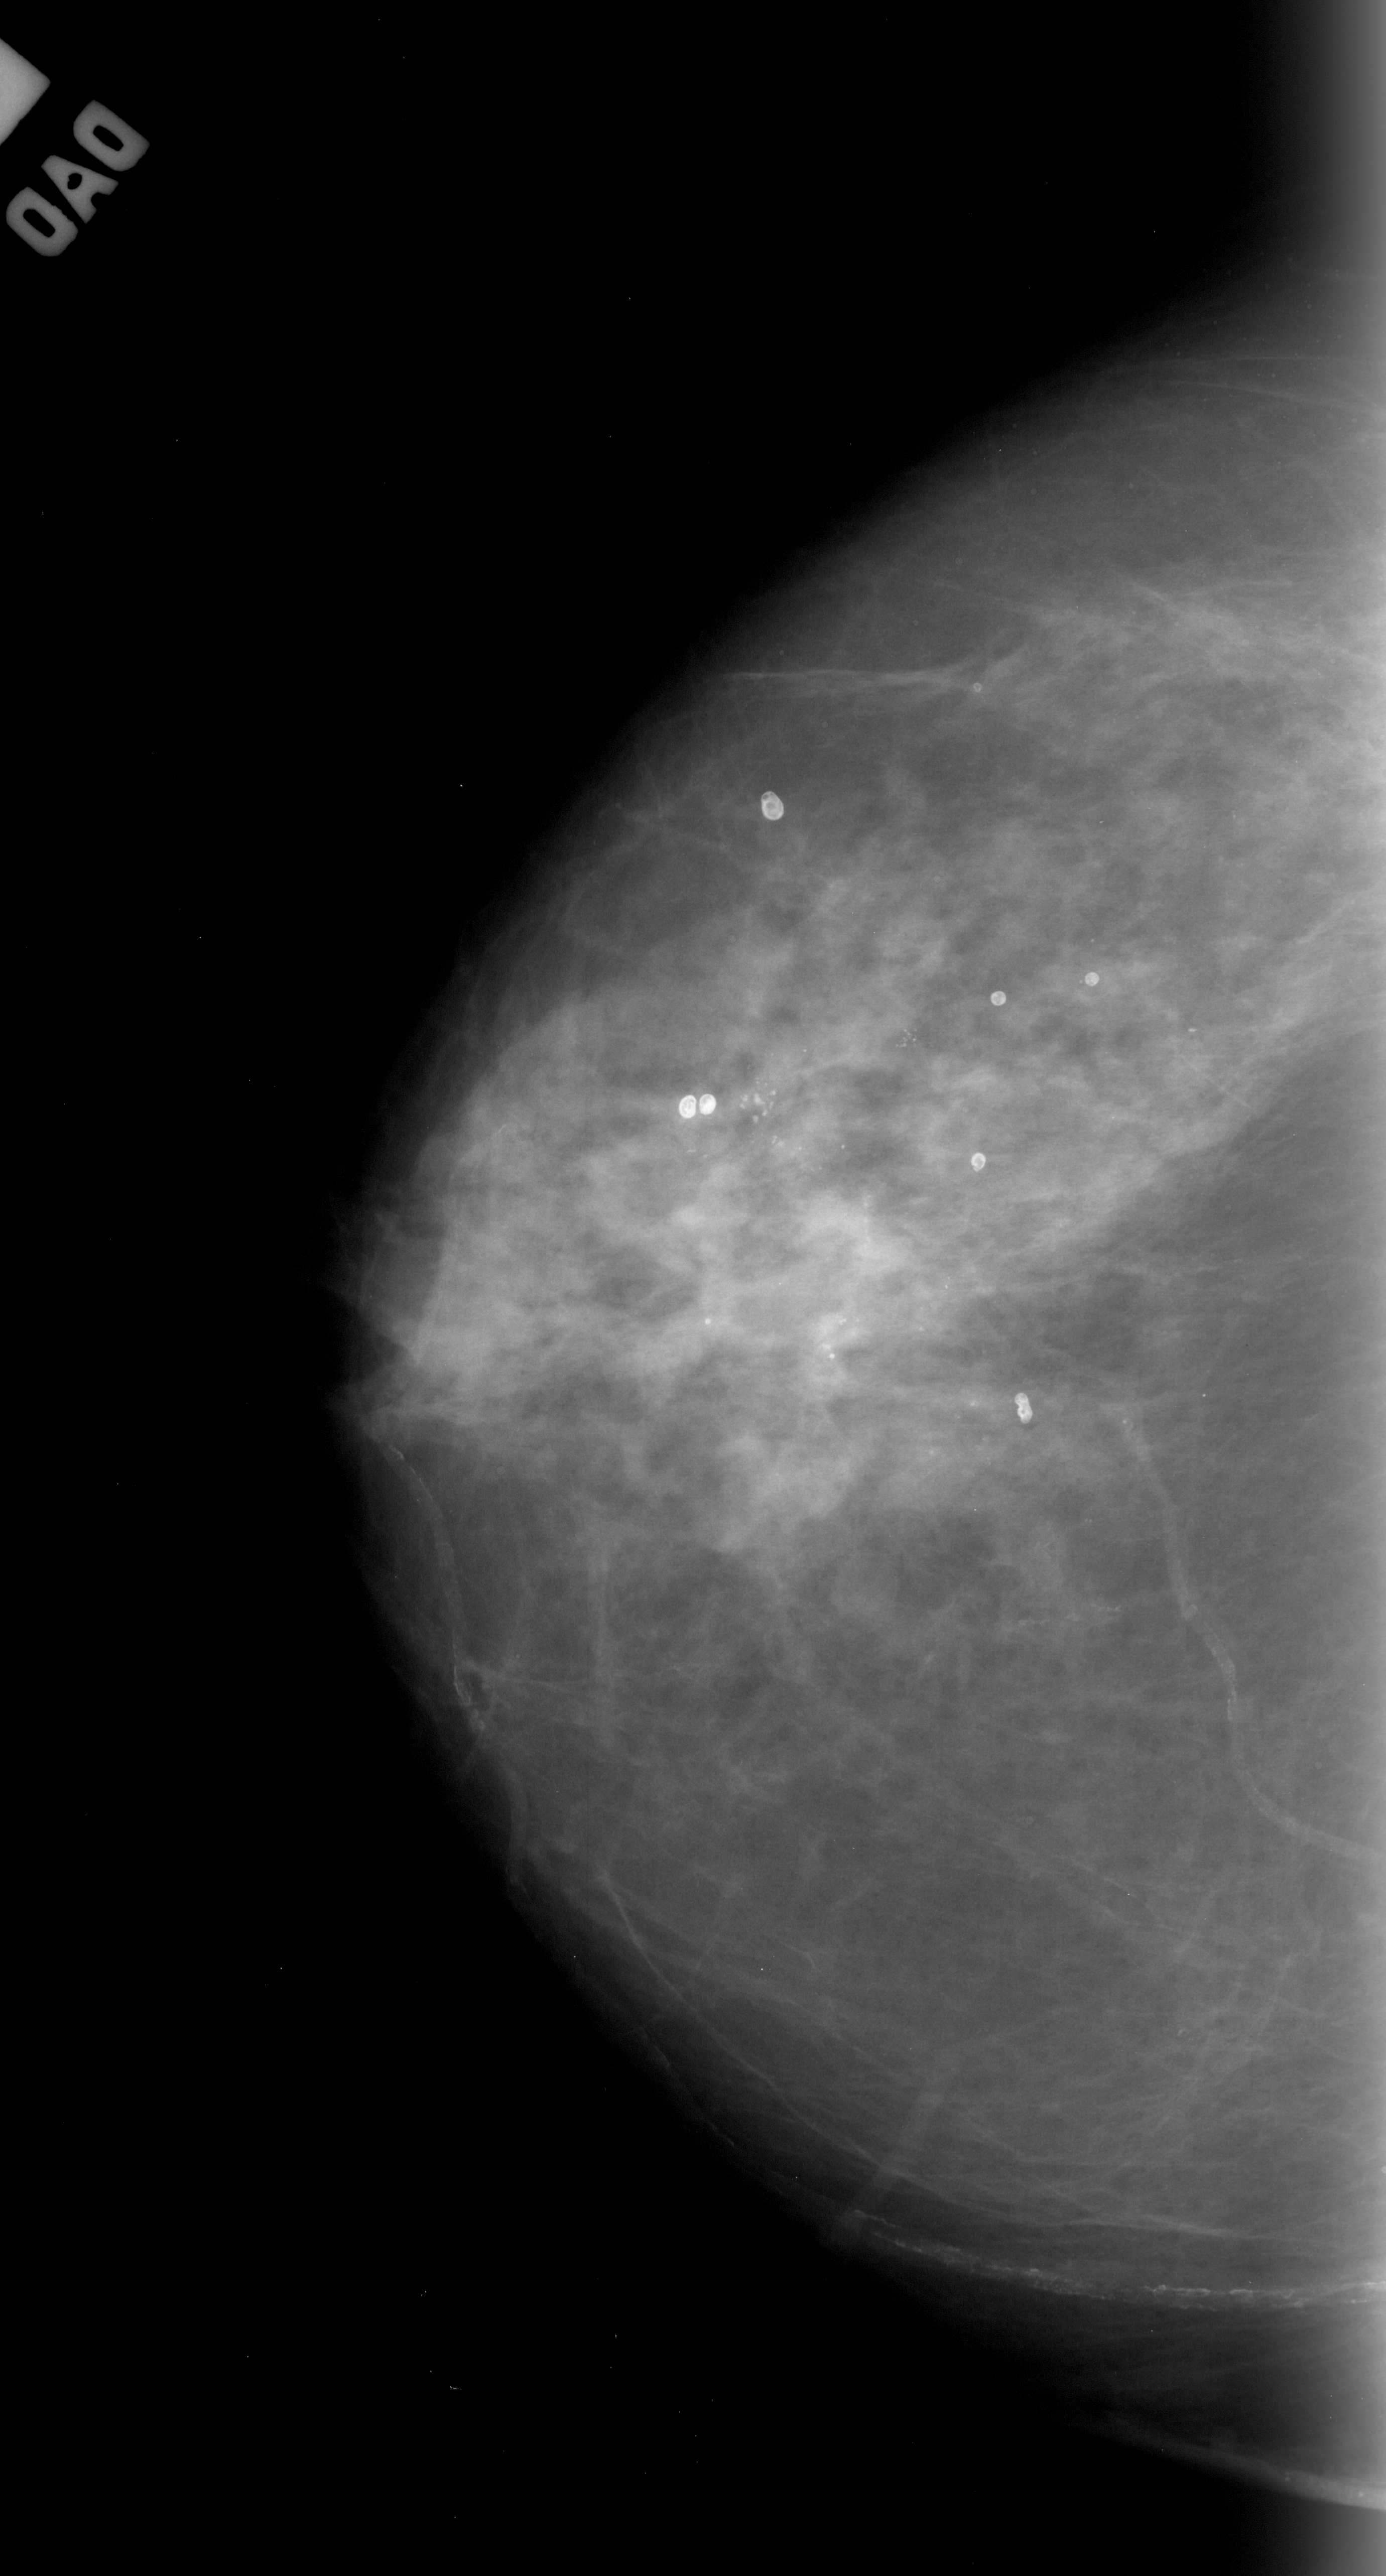
Mammogram (digitized film); left breast; craniocaudal (CC) view; breast composition: heterogeneously dense (BI-RADS density category 3 of 4); 1386 × 2576 image matrix.
Marked abnormalities (boxes around the expert regions of interest):
- calcifications, morphology pleomorphic, distribution segmental; BI-RADS assessment category 4; pathology (as recorded): malignant: box from (x=658, y=995) to (x=986, y=1425) px